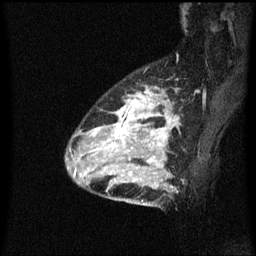
Breast MRI (dynamic contrast-enhanced), one sagittal slice; position 45 of 60 along the scan axis; dynamic contrast-enhanced series, image 2 of 3 at this slice position (ordered by acquisition); 1.5 T; TE 4.2 ms, TR 8.4 ms; 256 × 256 image matrix, field of view 200 × 200 mm. Female patient, age 34 years. From the clinical record (not read from this slice): setting: breast cancer imaged before/during neoadjuvant chemotherapy; receptor status: HR-positive, HER2-negative.
Structures marked on this image (semi-automatically segmented with operator editing):
- analysis volume of interest (the breast-tissue region the enhancement analysis was run in; not a lesion): box from (x=69, y=88) to (x=178, y=209) px
- tumour enhancement mask (voxels above the 70 % enhancement threshold inside the analysis volume of interest): (x=74, y=90)–(x=176, y=175)